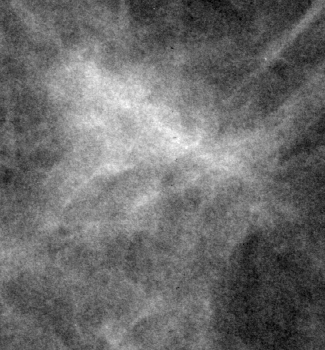
Region of interest cut from a scanned film mammogram (one marked finding); right breast; CC view.
- Finding: mass, shape irregular, margins ill defined; BI-RADS assessment category 5; pathology result (as recorded, not read from the image): malignant.